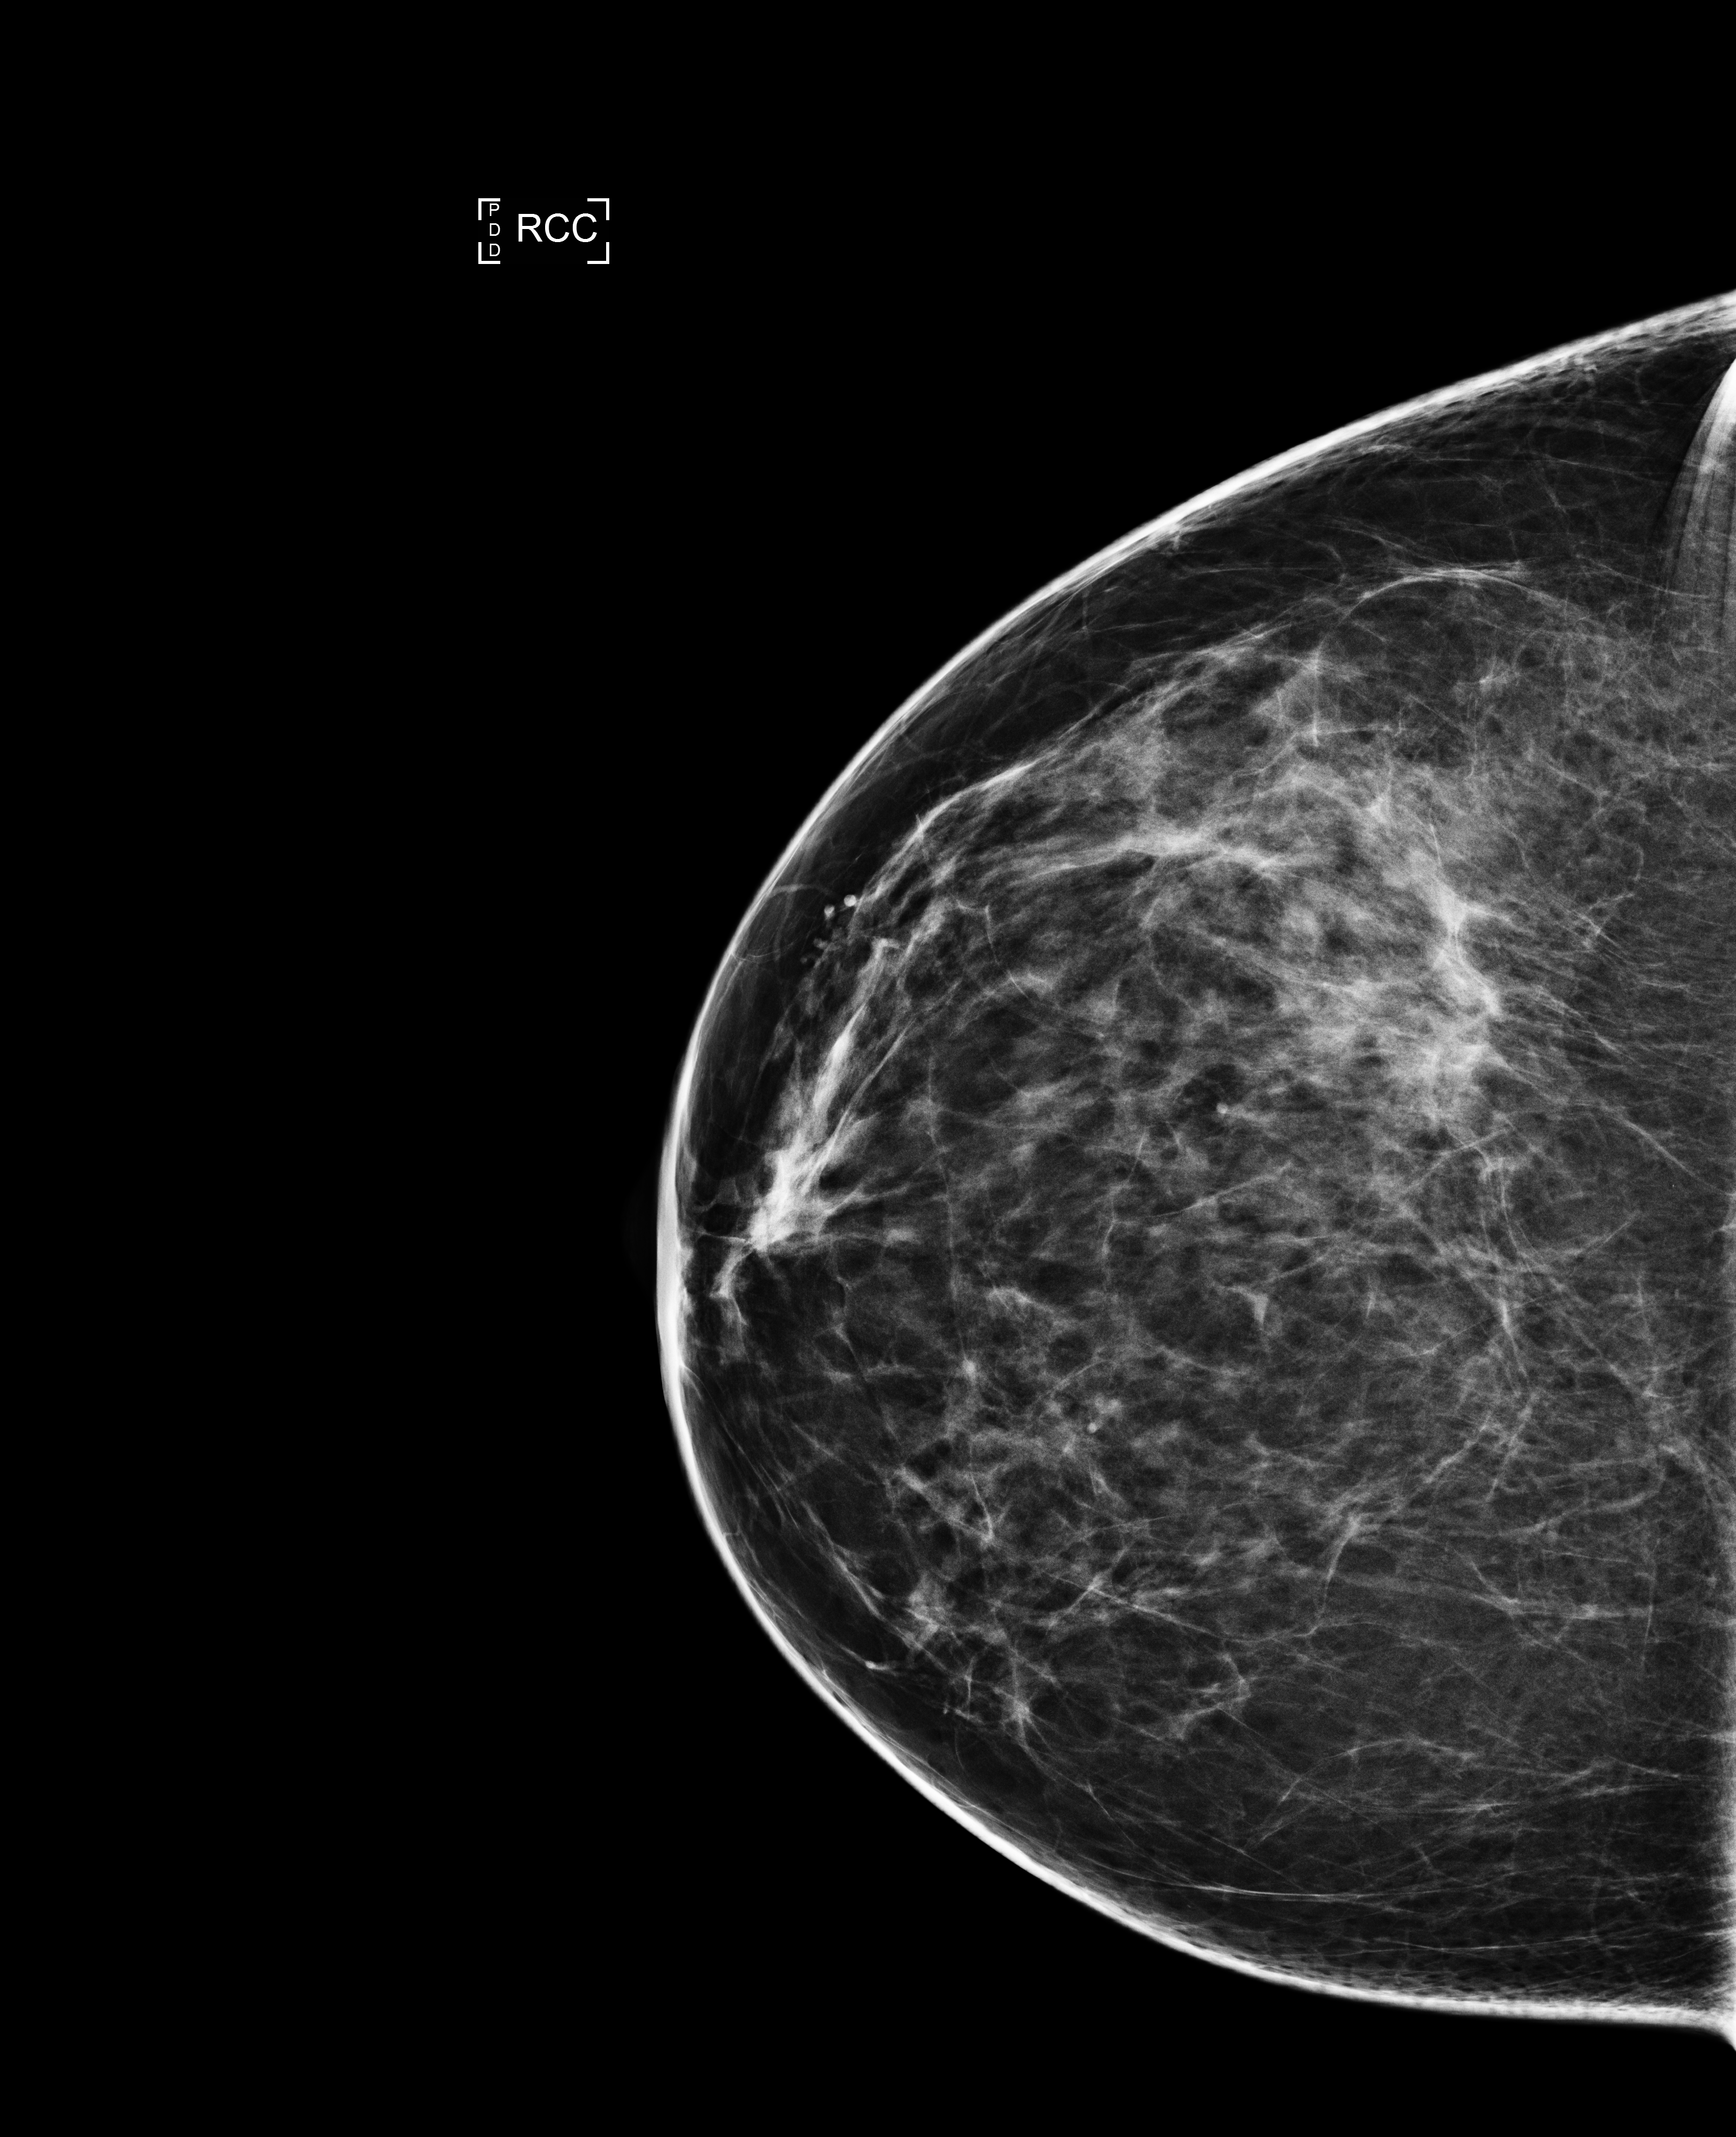
Screening examination. Female patient, age 51 years.
Image type: full-field digital mammogram. Breast: right. Projection: craniocaudal (CC) view.